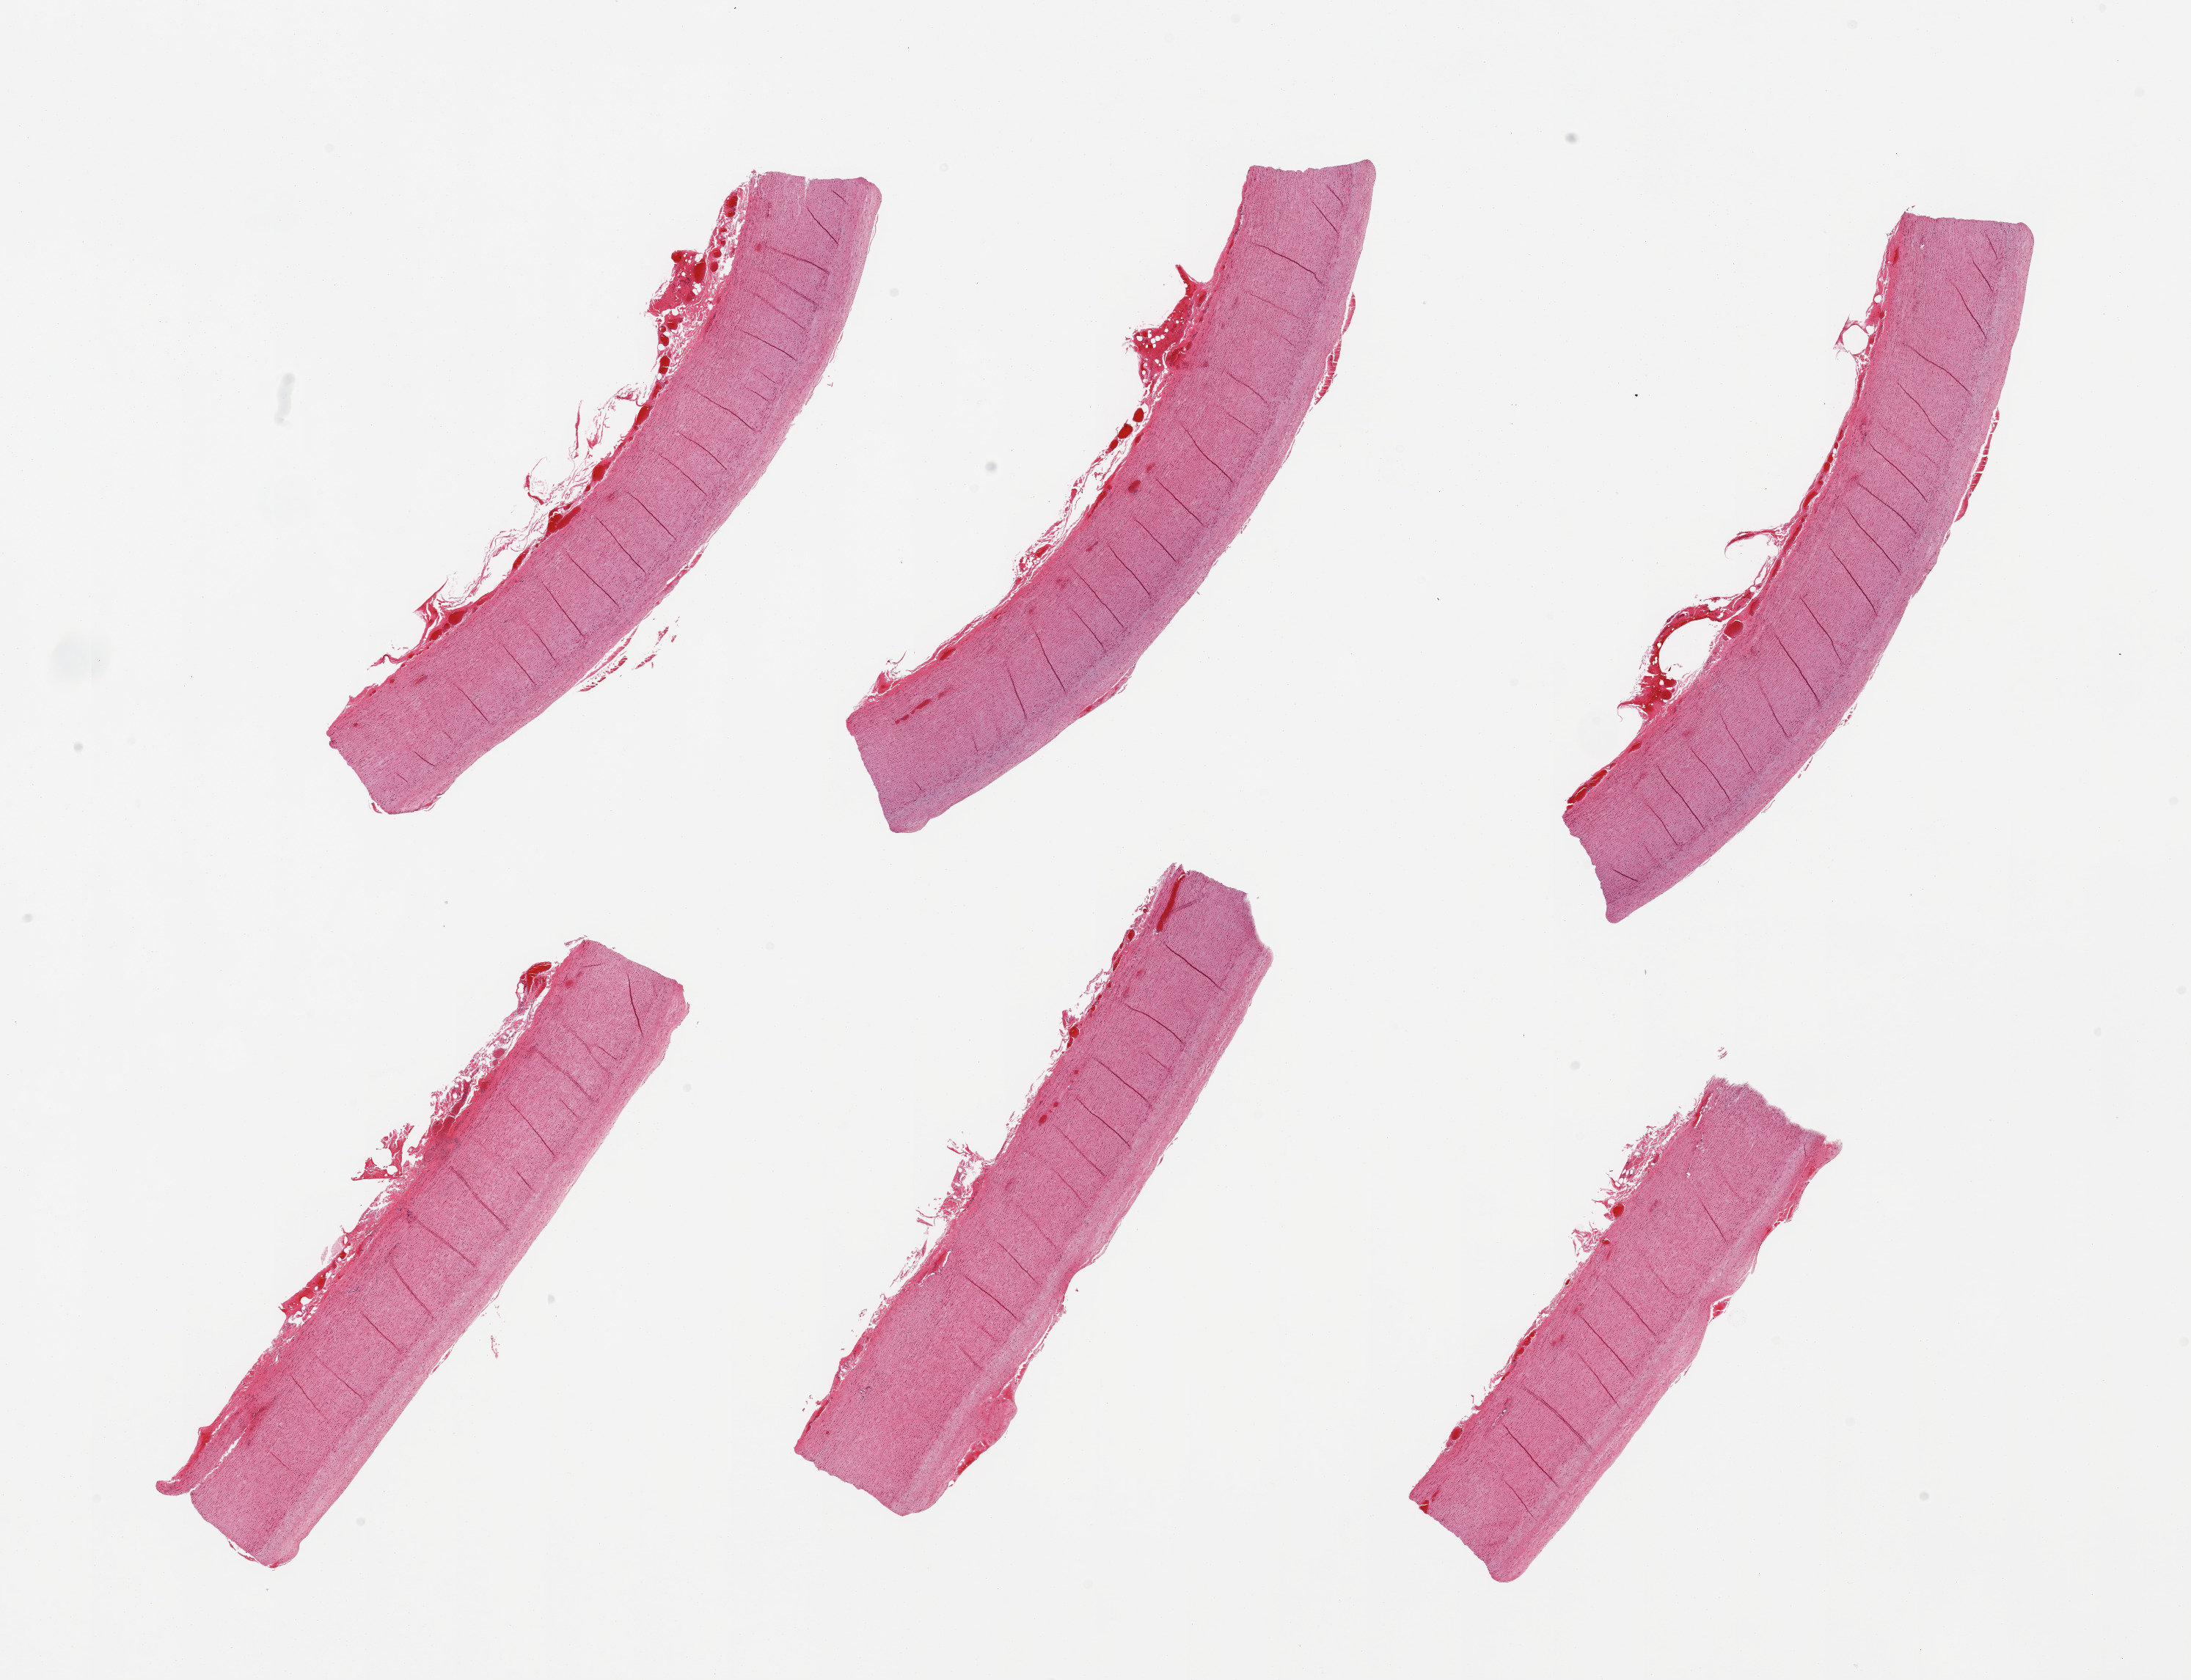
Digitized hematoxylin and eosin (H&E)-stained section, whole scanned area (about 23.6 x 18.1 mm) shown as a low-resolution overview, PAXgene-fixed, paraffin-embedded tissue, sampled site (target tissue): aorta, donor tissue sample.
Pathologist's review note for this sample: 6 pieces; no plaques; well trimmed.